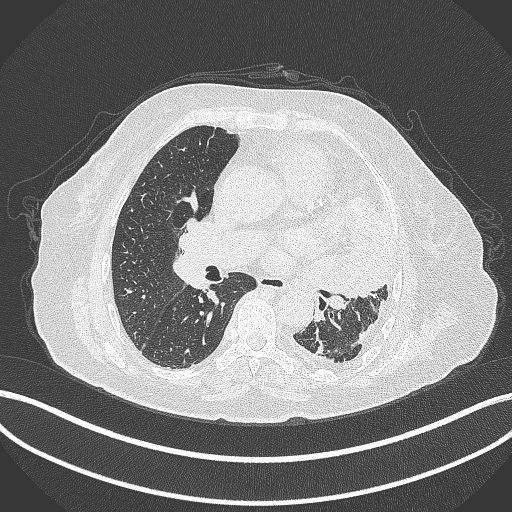
Chest CT, one axial slice. Slice 195 of 399 in the series (ordered by position). Reconstruction kernel B70f. Lung window (W 1500 / L -600 HU). 1 mm slice thickness. 512 × 512 image matrix. Patient: female, 75 years. Case-level facts recorded for this patient, not image findings: clinical TNM (as recorded): T3 N3 M1.
Annotated regions visible in this slice (rectangle marked by the reading radiologist):
- lung tumour (recorded histology: adenocarcinoma): box from (x=297, y=196) to (x=398, y=310) px